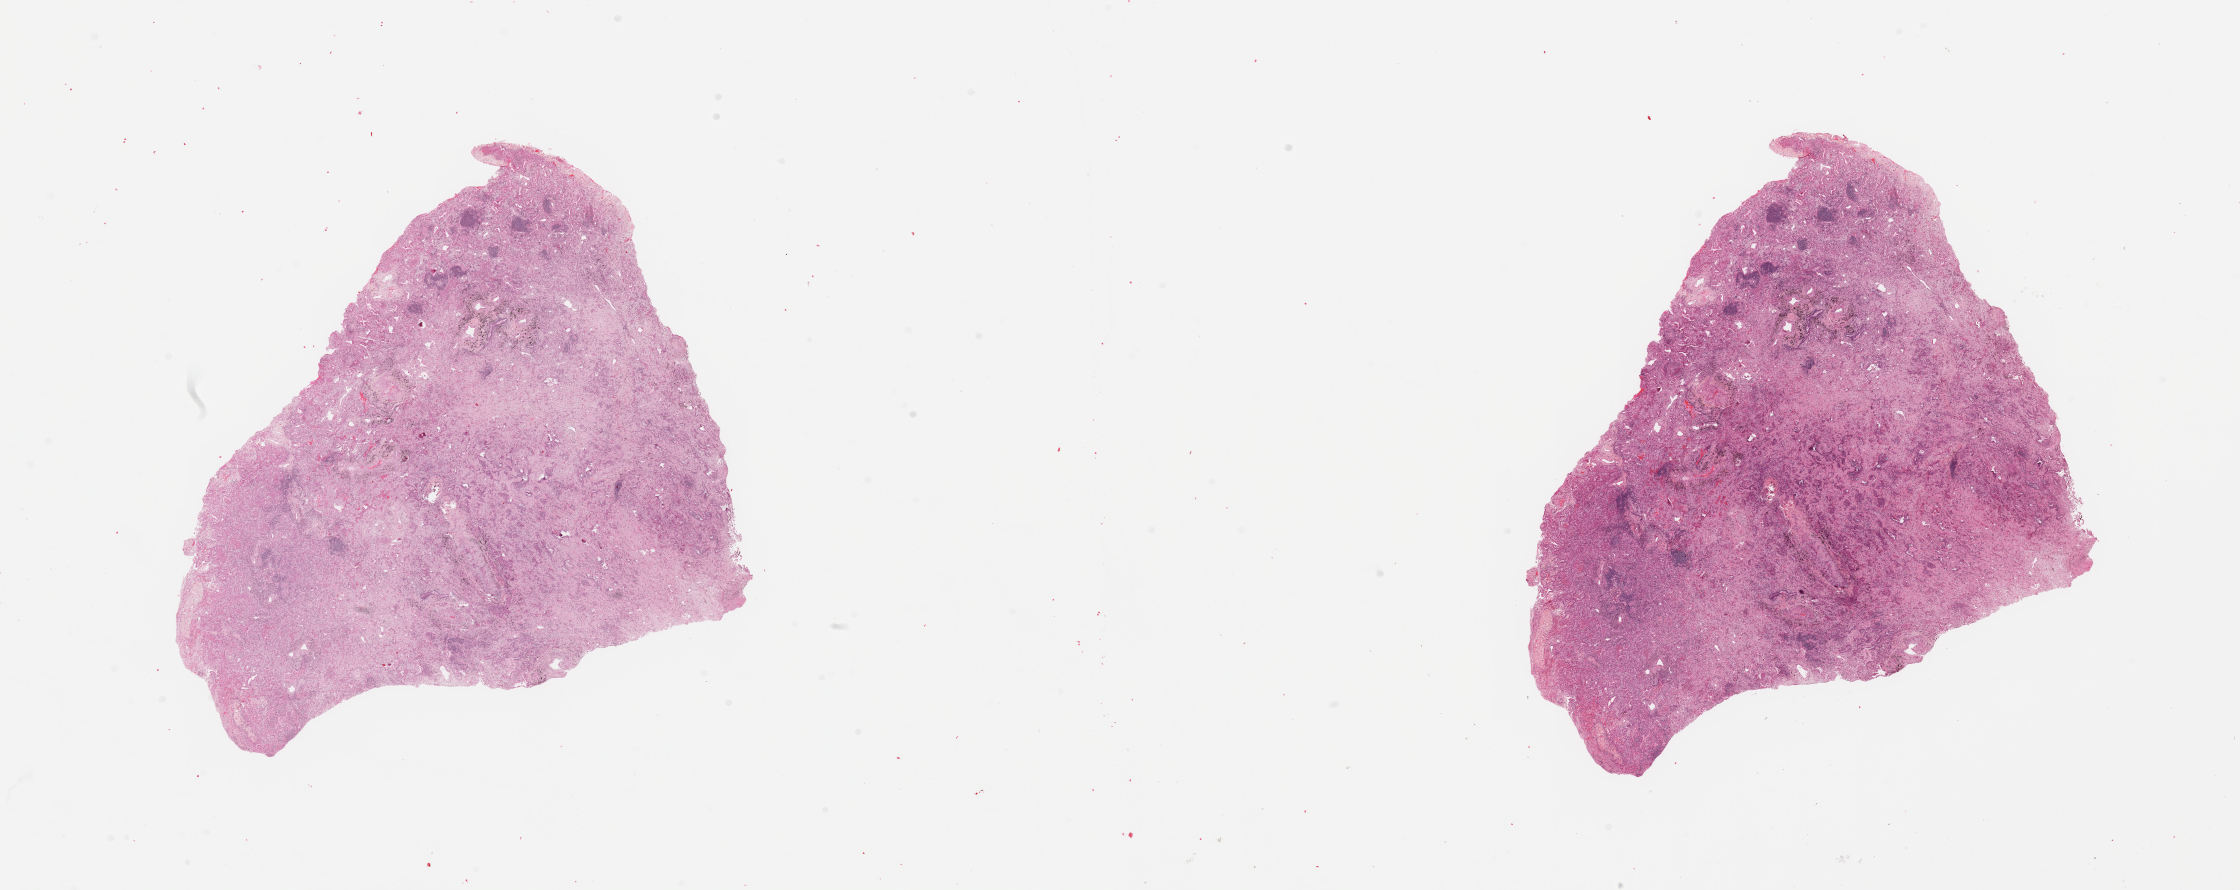
Whole-slide histology image, Hematoxylin and eosin (H&E) stained, a low-resolution overview of the entire scanned area, about 35.4 x 14.1 mm (from a 20x scan); lung, tumour tissue. 69-year-old female patient. Histologic grade: G2 (moderately differentiated).
- primary tumour site (as recorded): right upper lobe
- AJCC pathologic stage: IB
- histologic diagnosis: Adenocarcinoma, NOS